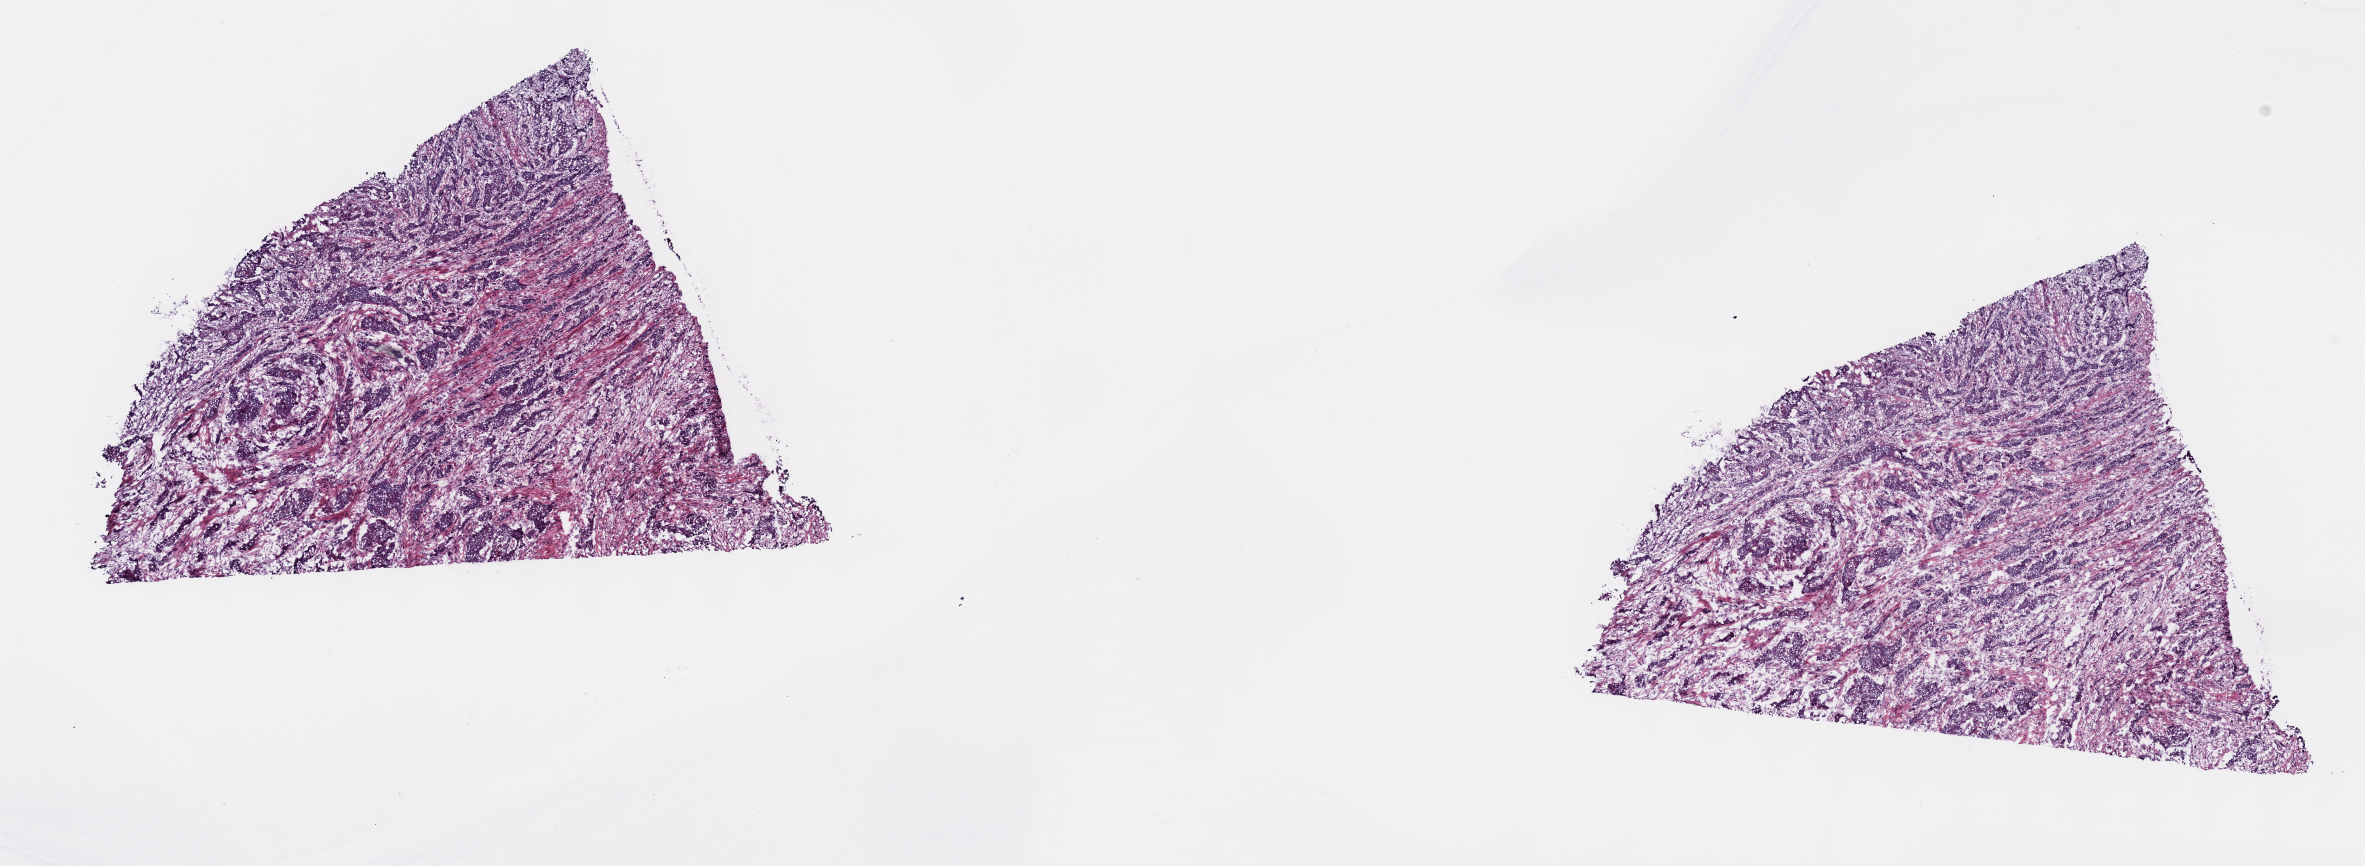
Whole-slide histology image, Hematoxylin and eosin (H&E) stained — shown as a low-resolution overview of the whole scanned area (about 19.1 x 7.0 mm, slide scanned at 40x), frozen section from the top of the tissue portion, esophagus, primary tumour sample. Patient: male, age at initial diagnosis 70 years. Slide review estimates, as recorded: tumour cells 100%, tumour nuclei 65%.
Pathologic diagnosis: Squamous cell carcinoma, NOS.